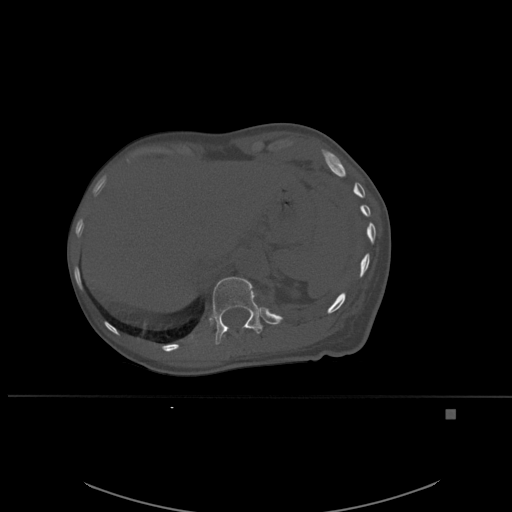
CT including the spine, one axial slice; position 284 of 537 along the scan axis; bone window (W 1800 / L 400 HU); 1.5 mm slice thickness; 512 × 512 image matrix, field of view 440 × 440 mm. Patient: female, 45 years. From the clinical record (not read from this slice): primary cancer: lung.
Annotated regions visible in this slice (semi-automatically segmented with operator editing):
- T11 vertebra: bounding box <221,335,225,339> (left, top, right, bottom; pixels)
- T12 vertebra: <212,277,263,345>